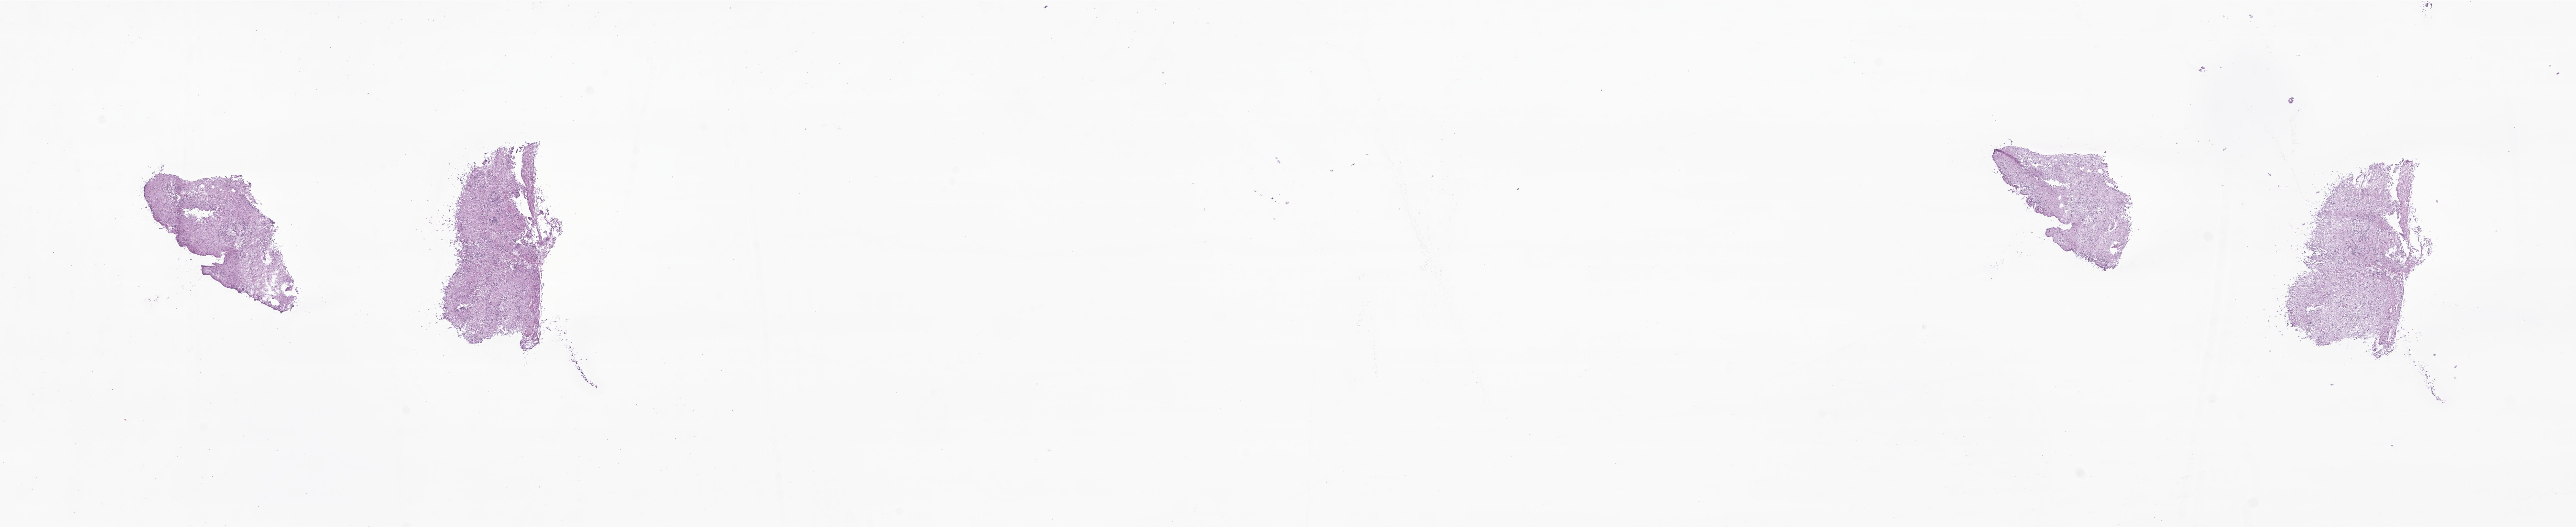
Haematoxylin and eosin whole-slide image of tumor tissue from the brain, shown as a low-resolution overview of the whole scanned area (about 33.6 x 6.9 mm), cryosection (OCT / tissue freezing medium). Patient male; age 34 months (2 years 10 months).
* diagnosis (ICD-O-3 morphology term): Ependymoma, NOS